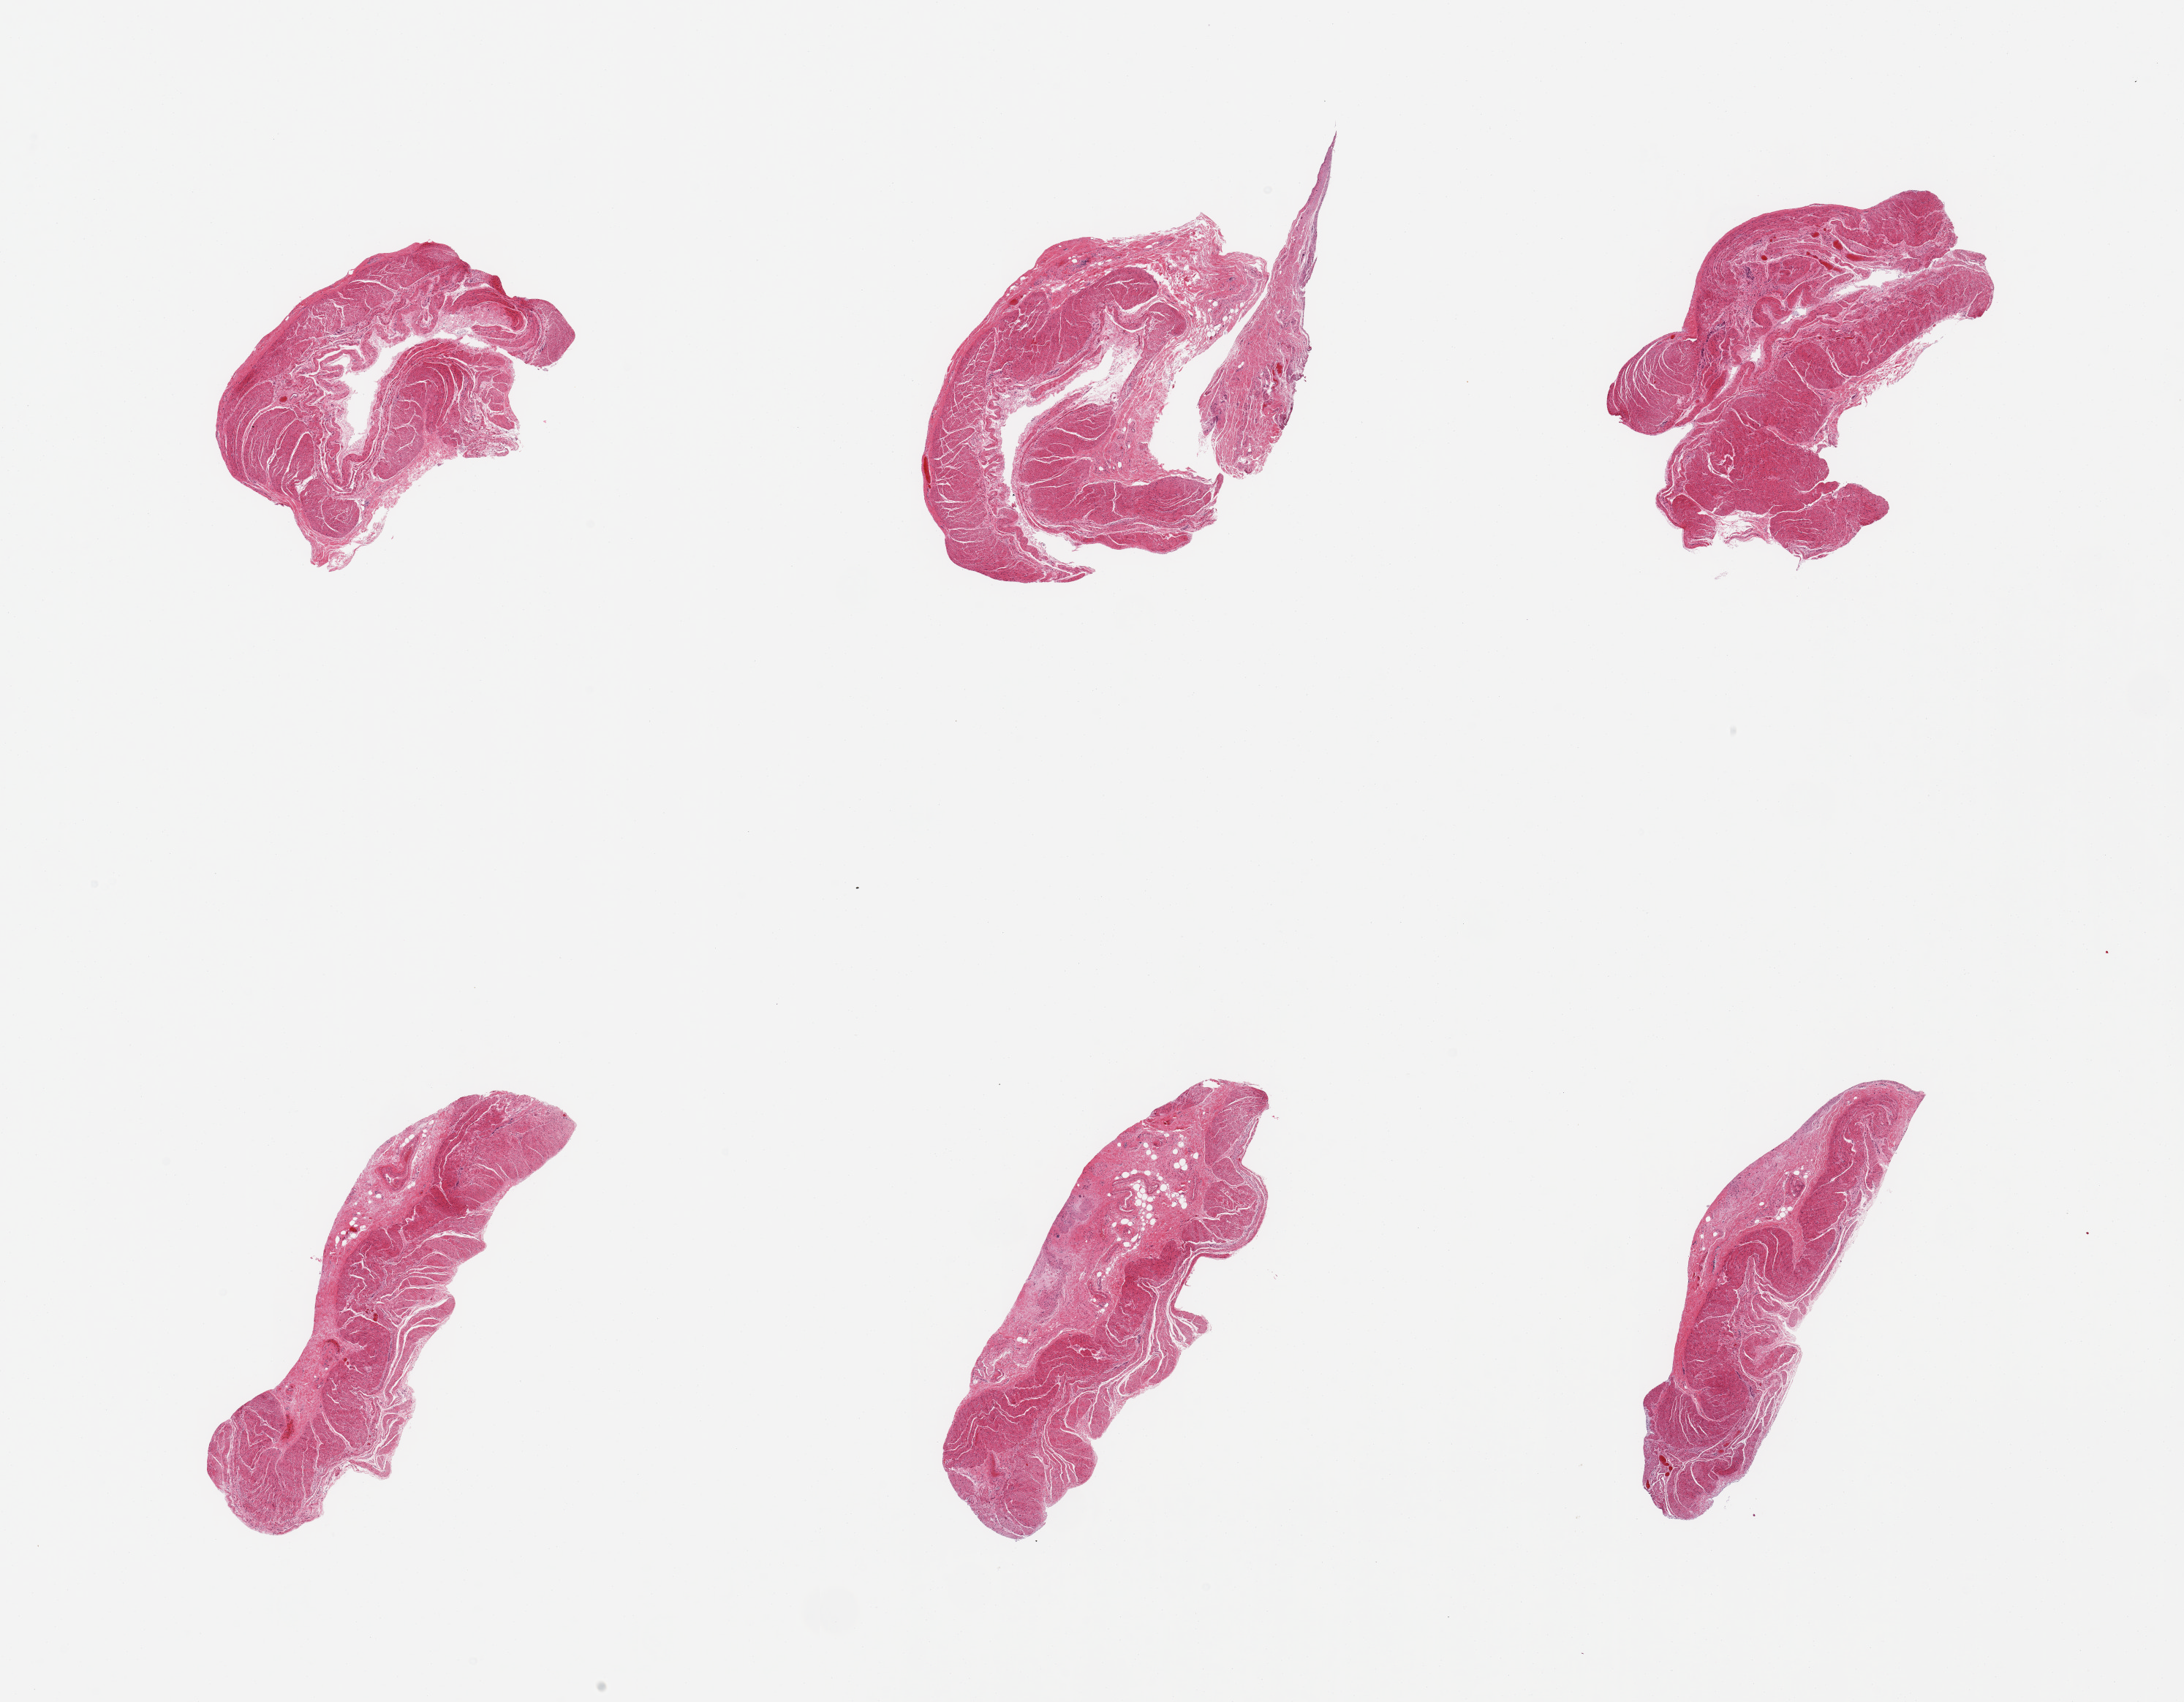
Haematoxylin and eosin whole-slide image, brightfield — low-resolution overview of the scanned area, about 23.6 x 18.4 mm (slide scanned at 20x). PAXgene-fixed, paraffin-embedded tissue. Target tissue: sigmoid colon. Donor tissue sample. Donor: male.
Review note (as recorded): 6 pieces, confirmed target muscularis.